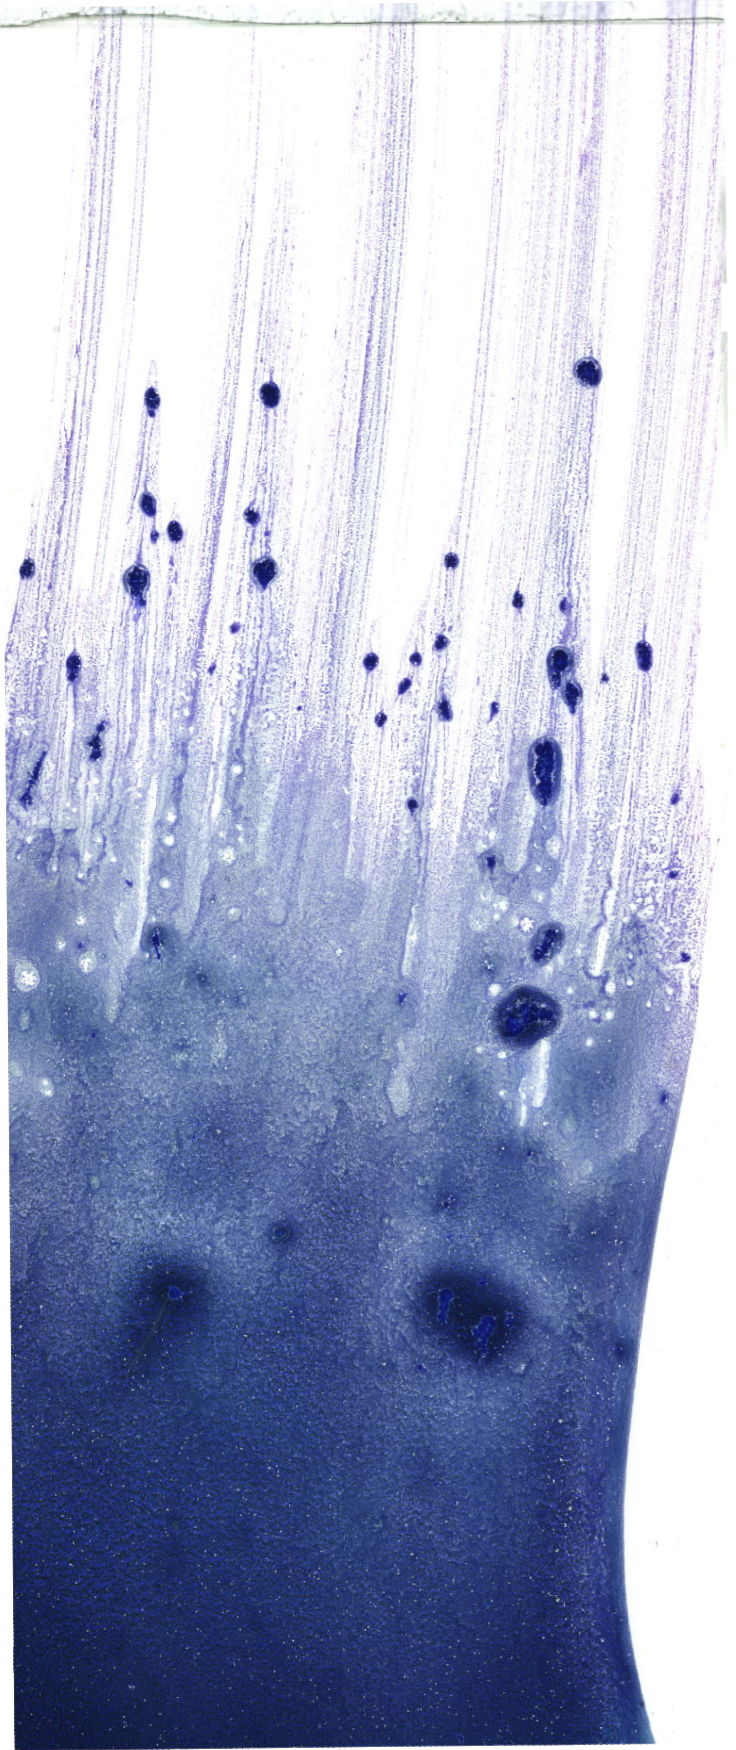
Bone marrow aspirate smear, May-Grünwald-Giemsa (MGG) stain, whole-slide image — whole scanned area (about 20.9 x 49.6 mm) shown as a low-resolution overview. Patient sex: male.
Diagnosis: B Acute Lymphoblastic Leukemia.